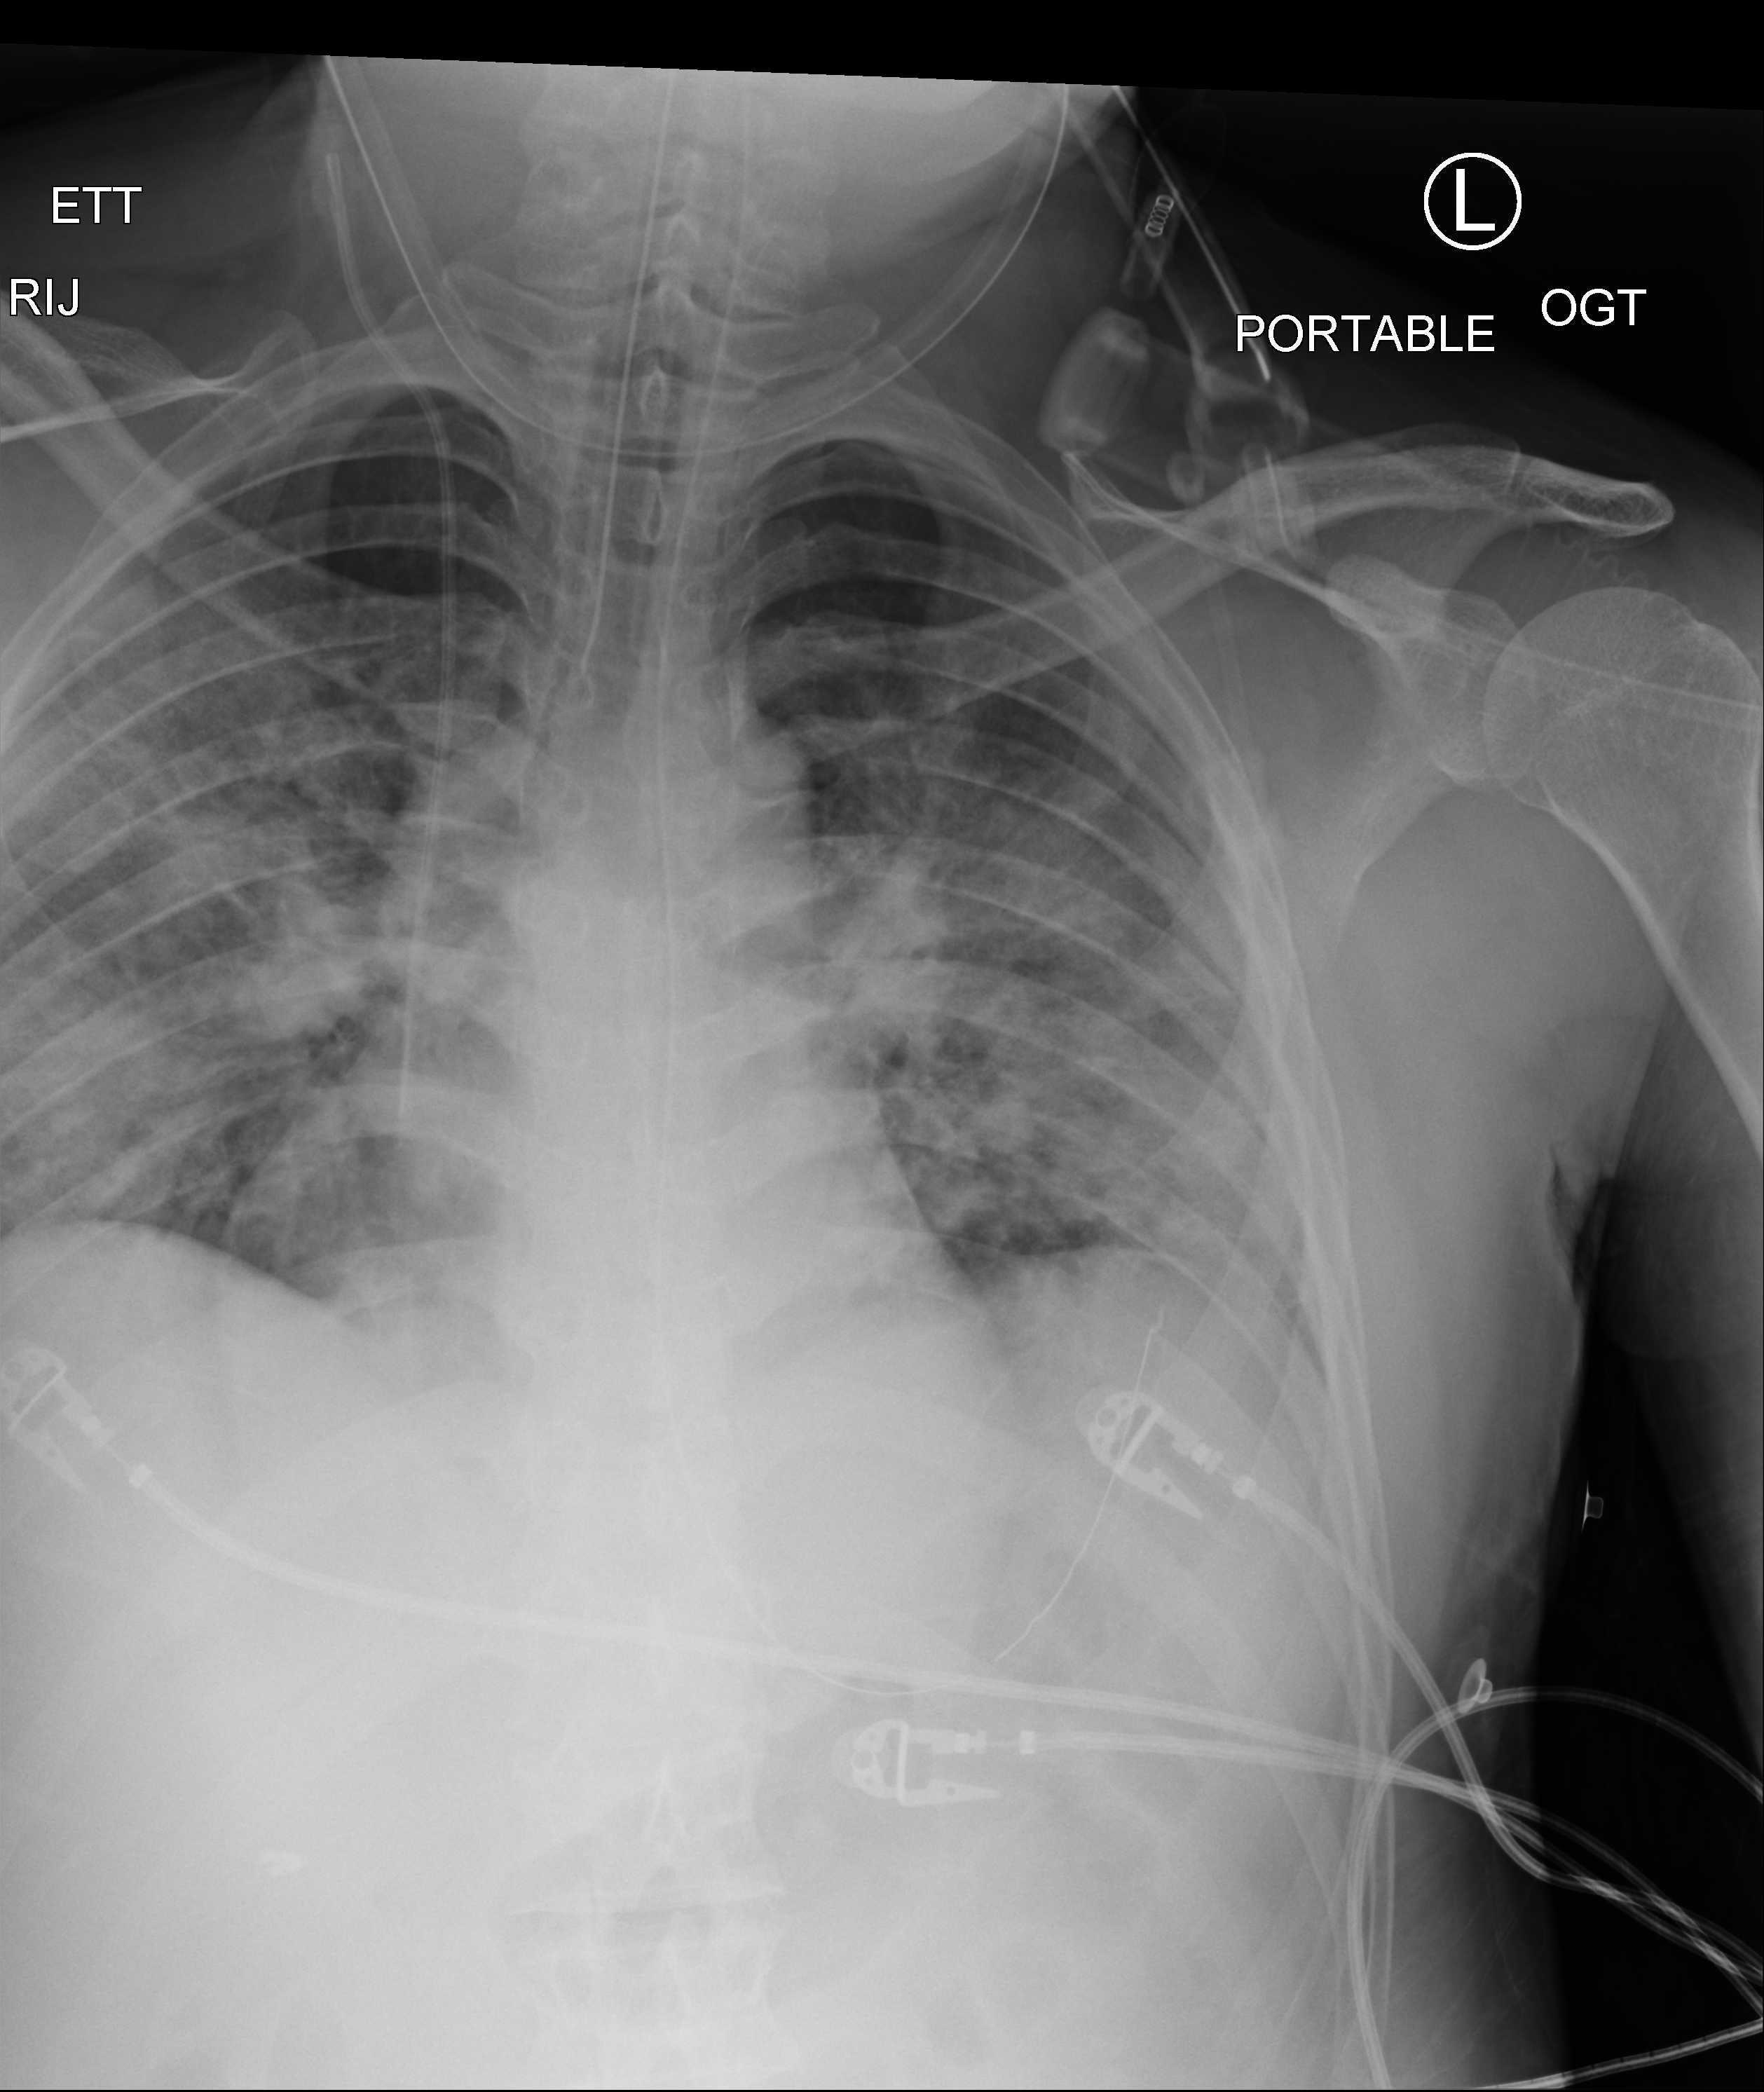
Portable chest radiograph; anteroposterior (AP) projection. Patient hospitalised with COVID-19; male, aged 18–59 years.
From the hospital-stay record, not from the radiograph (when in the stay this image was taken is not recorded):
- admitted to intensive care during this hospital stay: yes
- COPD (admission record): no